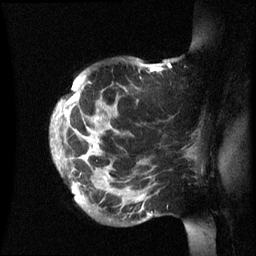
Breast MRI (dynamic contrast-enhanced), one sagittal slice; slice 48 of 60 in the series (ordered by position); dynamic contrast-enhanced series, image 2 of 3 at this slice position (ordered by acquisition); 1.5 T; TE 4.2 ms, TR 8.4 ms; 2.4 mm slice thickness; 256 × 256 image matrix, field of view 230 × 230 mm. Patient: female, 48 years.
Outlined on this slice (semi-automatic segmentation, software-assisted and operator-edited):
- analysis volume of interest (the breast-tissue region the enhancement analysis was run in; not a lesion): bounding box [x1, y1, x2, y2] px = [51, 59, 202, 236]
- tumour enhancement mask (voxels above the 70 % enhancement threshold inside the analysis volume of interest): [55, 64, 161, 192]